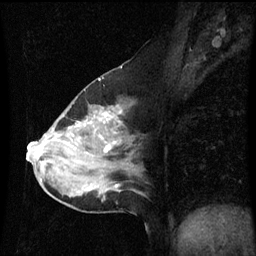
Breast MRI (dynamic contrast-enhanced), one sagittal slice. Slice 33 of 60 in the series (ordered by position). Dynamic contrast-enhanced series, image 2 of 3 at this slice position (ordered by acquisition). 1.5 T. TE 4.2 ms, TR 8.9 ms. 2 mm slice thickness. 256 × 256 image matrix, field of view 200 × 200 mm. Female patient, age 50 years. From the clinical record (not read from this slice): setting: breast cancer imaged before/during neoadjuvant chemotherapy; receptor status: HR-positive, HER2-negative.
Annotated regions visible in this slice (semi-automatically segmented with operator editing):
- analysis volume of interest (the breast-tissue region the enhancement analysis was run in; not a lesion): bounding box <33,90,139,209> (left, top, right, bottom; pixels)
- tumour enhancement mask (voxels above the 70 % enhancement threshold inside the analysis volume of interest): <33,114,113,153>